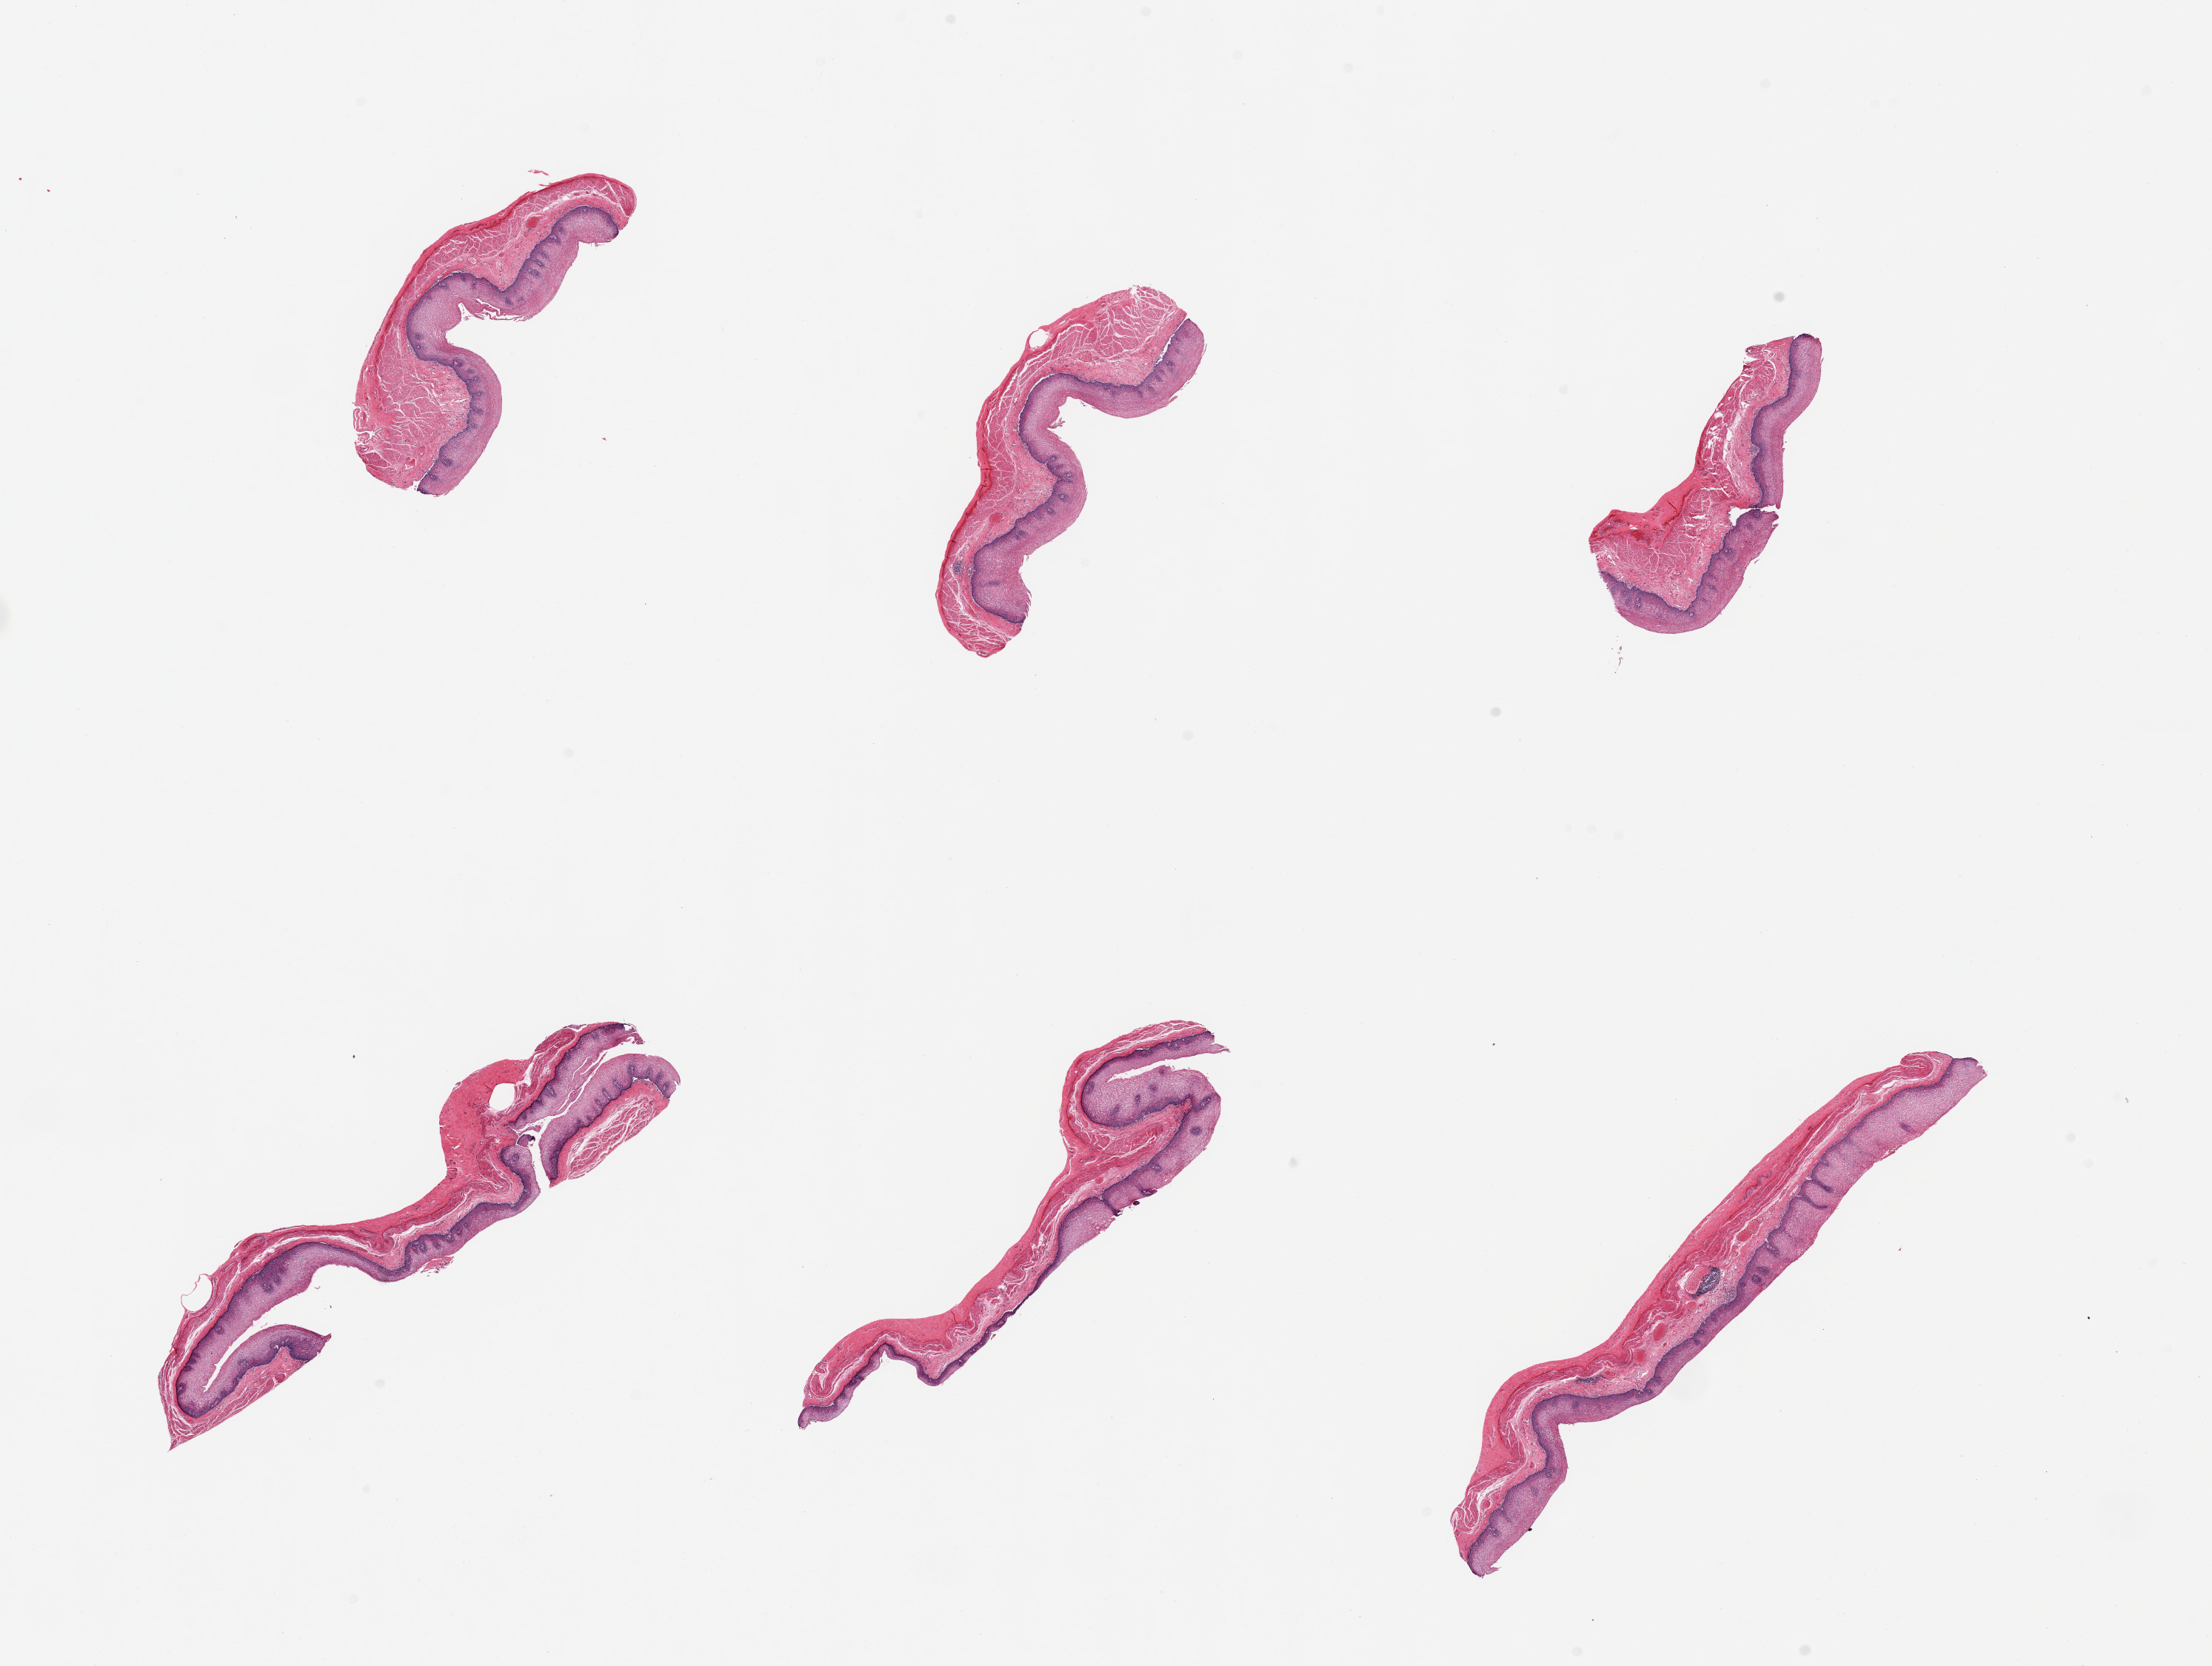
Whole-slide image, hematoxylin and eosin (H&E) stain — shown as a low-resolution overview of the whole scanned area (about 23.6 x 17.8 mm); PAXgene-fixed, paraffin-embedded tissue; section of esophageal mucous membrane (target tissue); tissue donor sample. Female donor.
Pathologist's review note for this sample: 6 pieces, squamous mucosa is ~20% thickness.